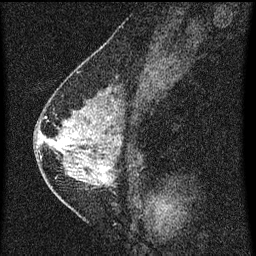
Breast MRI (dynamic contrast-enhanced), one sagittal slice. Slice 28 of 60 in the series (ordered by position). Dynamic contrast-enhanced series, image 2 of 3 at this slice position (ordered by acquisition). 1.5 T. TE 4.2 ms, TR 8 ms. 2 mm slice thickness. 256 × 256 image matrix. Patient: female, 47 years.
Structures marked on this image (semi-automatic segmentation, software-assisted and operator-edited):
- analysis volume of interest (the breast-tissue region the enhancement analysis was run in; not a lesion): box from (x=42, y=92) to (x=140, y=199) px
- tumour enhancement mask (voxels above the 70 % enhancement threshold inside the analysis volume of interest): (x=42, y=116)–(x=111, y=177)